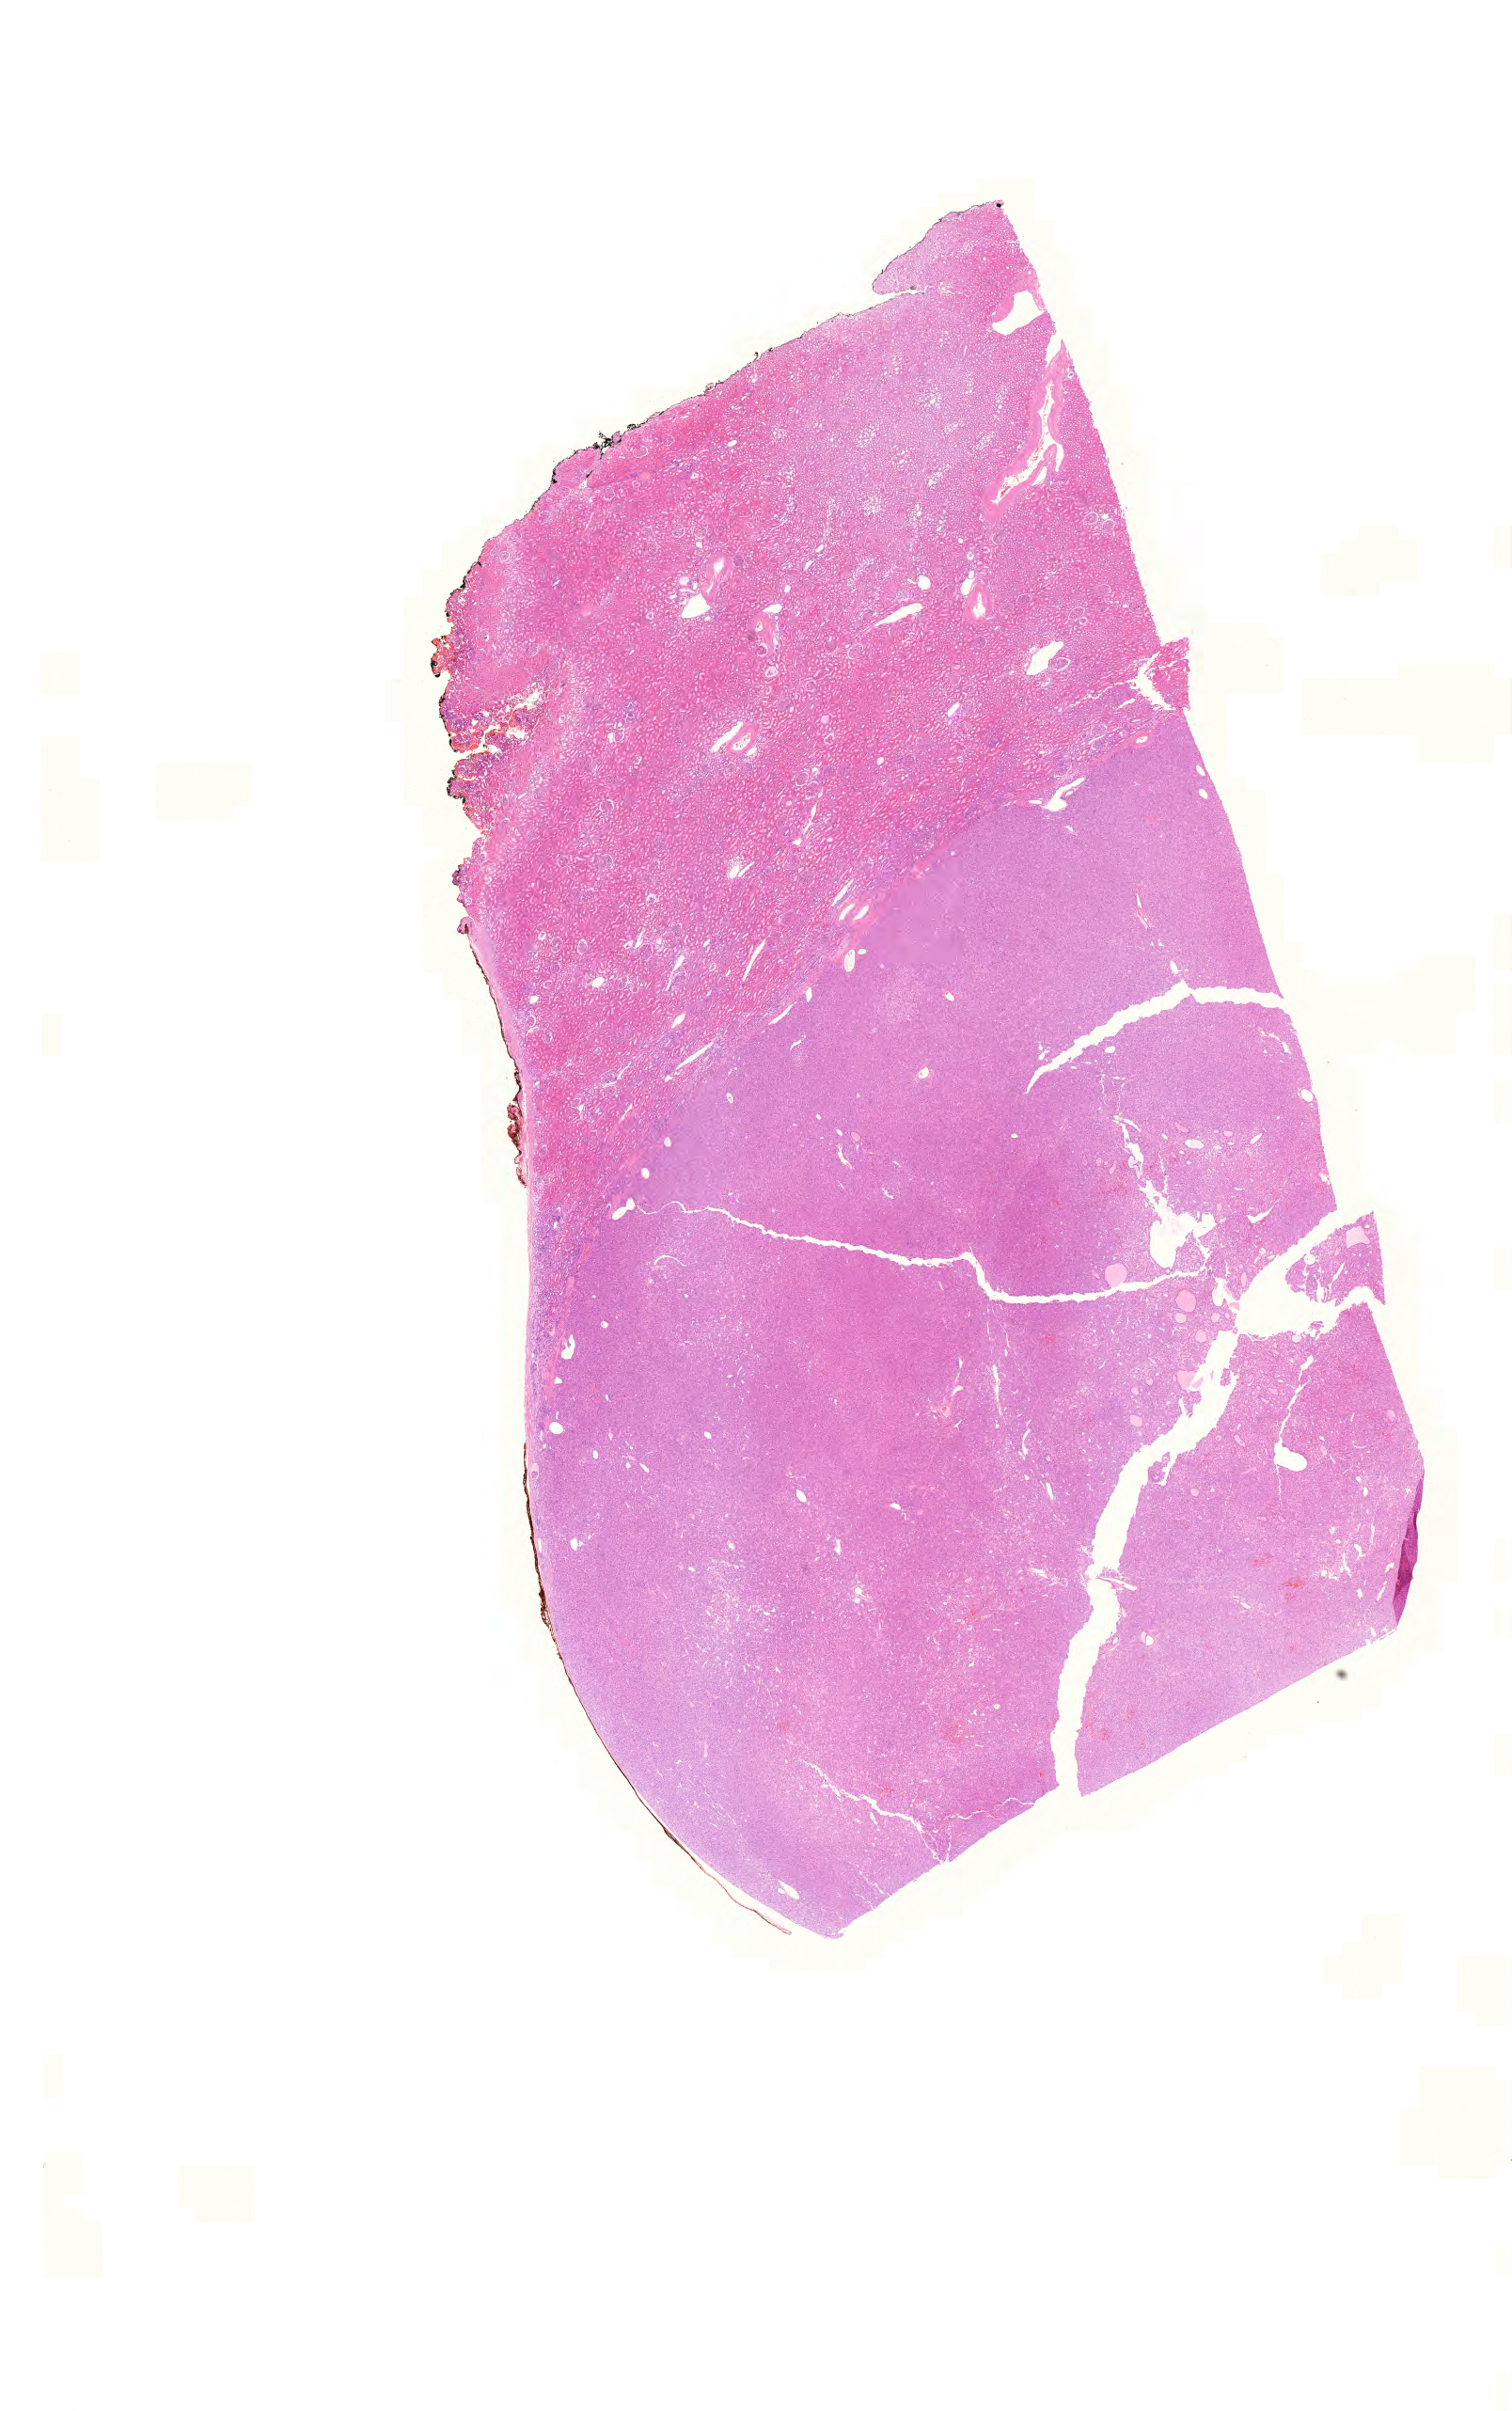
Whole-slide histology image, H&E-stained, whole scanned area (about 23.9 x 38.2 mm) shown as a low-resolution overview. FFPE section. Sample: primary tumour, kidney. Female patient; age at initial diagnosis 47 years. Histologic grade: G1 (well differentiated).
Histologic diagnosis: Clear cell adenocarcinoma, NOS. AJCC pathologic stage: I (7th edition). Laterality: right.